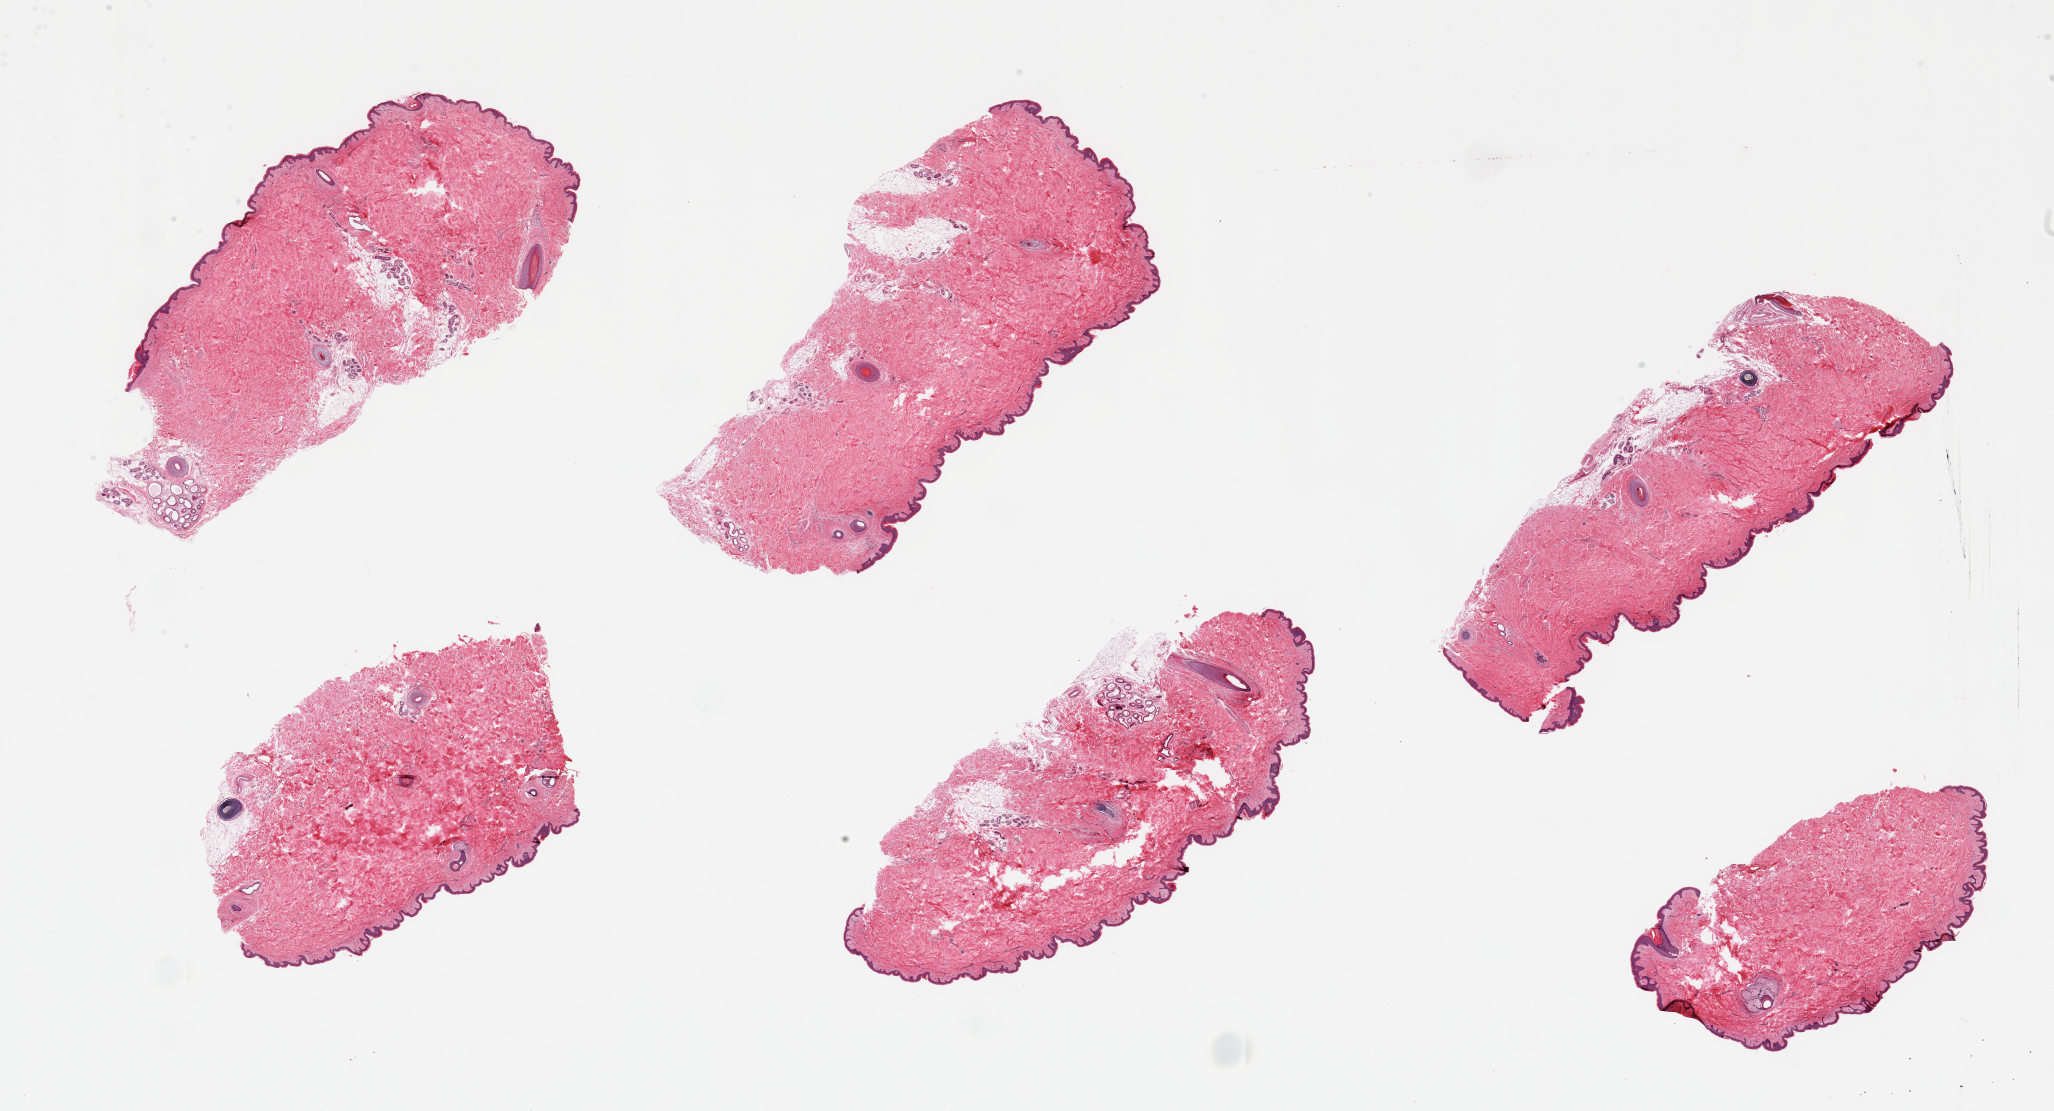
Whole-slide image, haematoxylin and eosin stain — whole scanned area (about 32.5 x 17.6 mm) shown as a low-resolution overview. PAXgene-fixed paraffin-embedded (PFPE) section. Sampled site (target tissue): skin of suprapubic region. Tissue donor sample. Donor: male.
Review note (as recorded): 6 pieces; up to 10% attached and periadnexal fat.